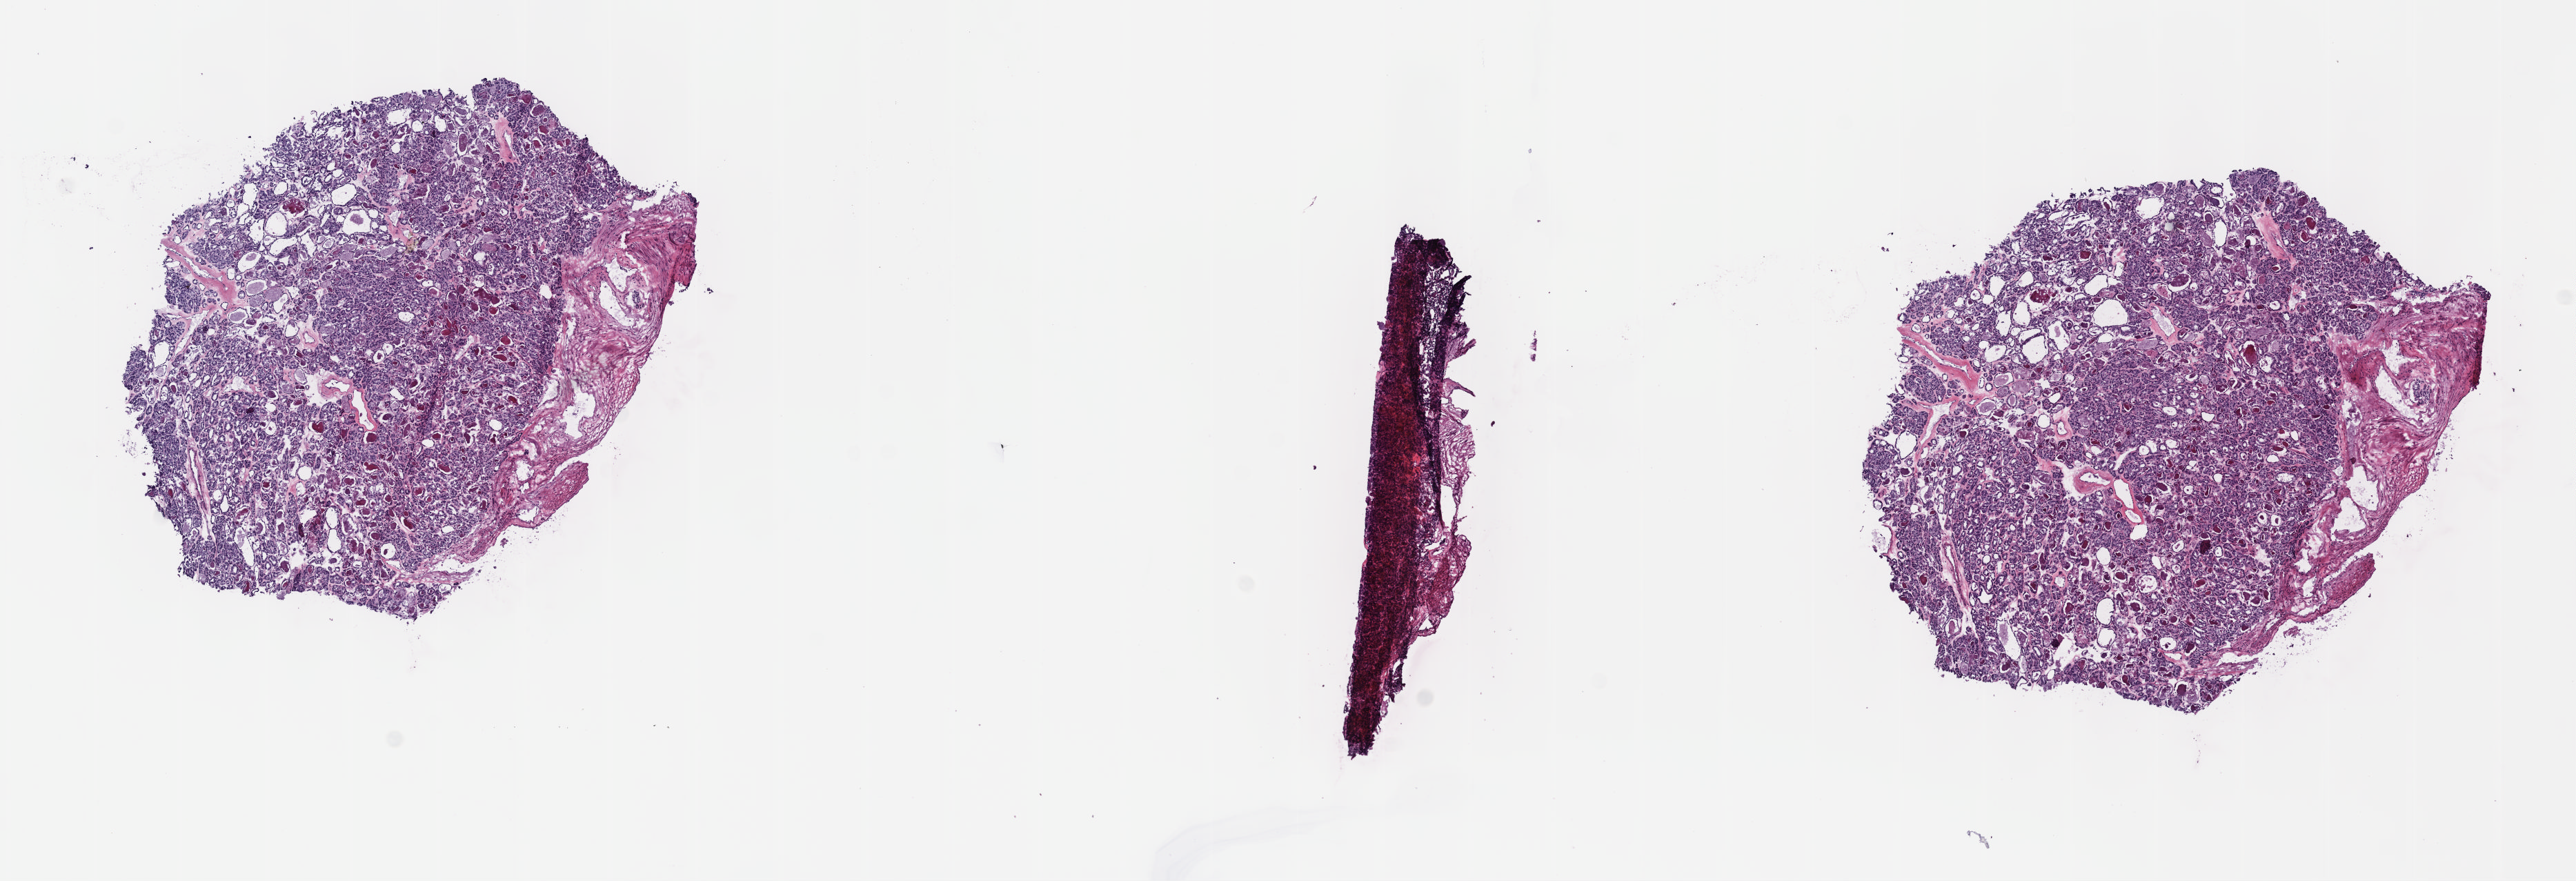
Digitized H&E tissue section (whole slide), whole scanned area (about 15.1 x 5.2 mm) shown as a low-resolution overview. Frozen section from the top of the tissue portion. Primary tumour sample from the thyroid. Male, age 74 years at initial diagnosis.
Pathologic diagnosis: Papillary carcinoma, follicular variant (thyroid gland).